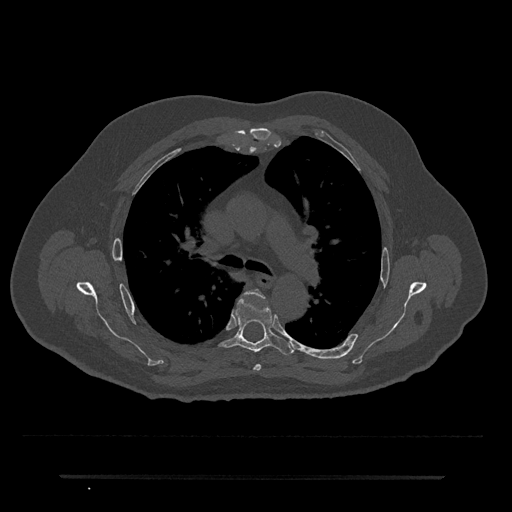
CT including the spine, one axial slice; slice 490 of 797 in the series (ordered by position); reconstruction kernel Br40s/3; 120 kVp; bone window (W 1800 / L 400 HU); 0.5 mm slice thickness; 512 × 512 image matrix. Male patient, age 69 years. Case-level facts recorded for this patient, not image findings: primary cancer: prostate.
Outlined on this slice (semi-automatically segmented with operator editing):
- T4 vertebra: bounding box (x1, y1, x2, y2) in pixels: (243, 289, 266, 371)
- T5 vertebra: (220, 294, 294, 355)